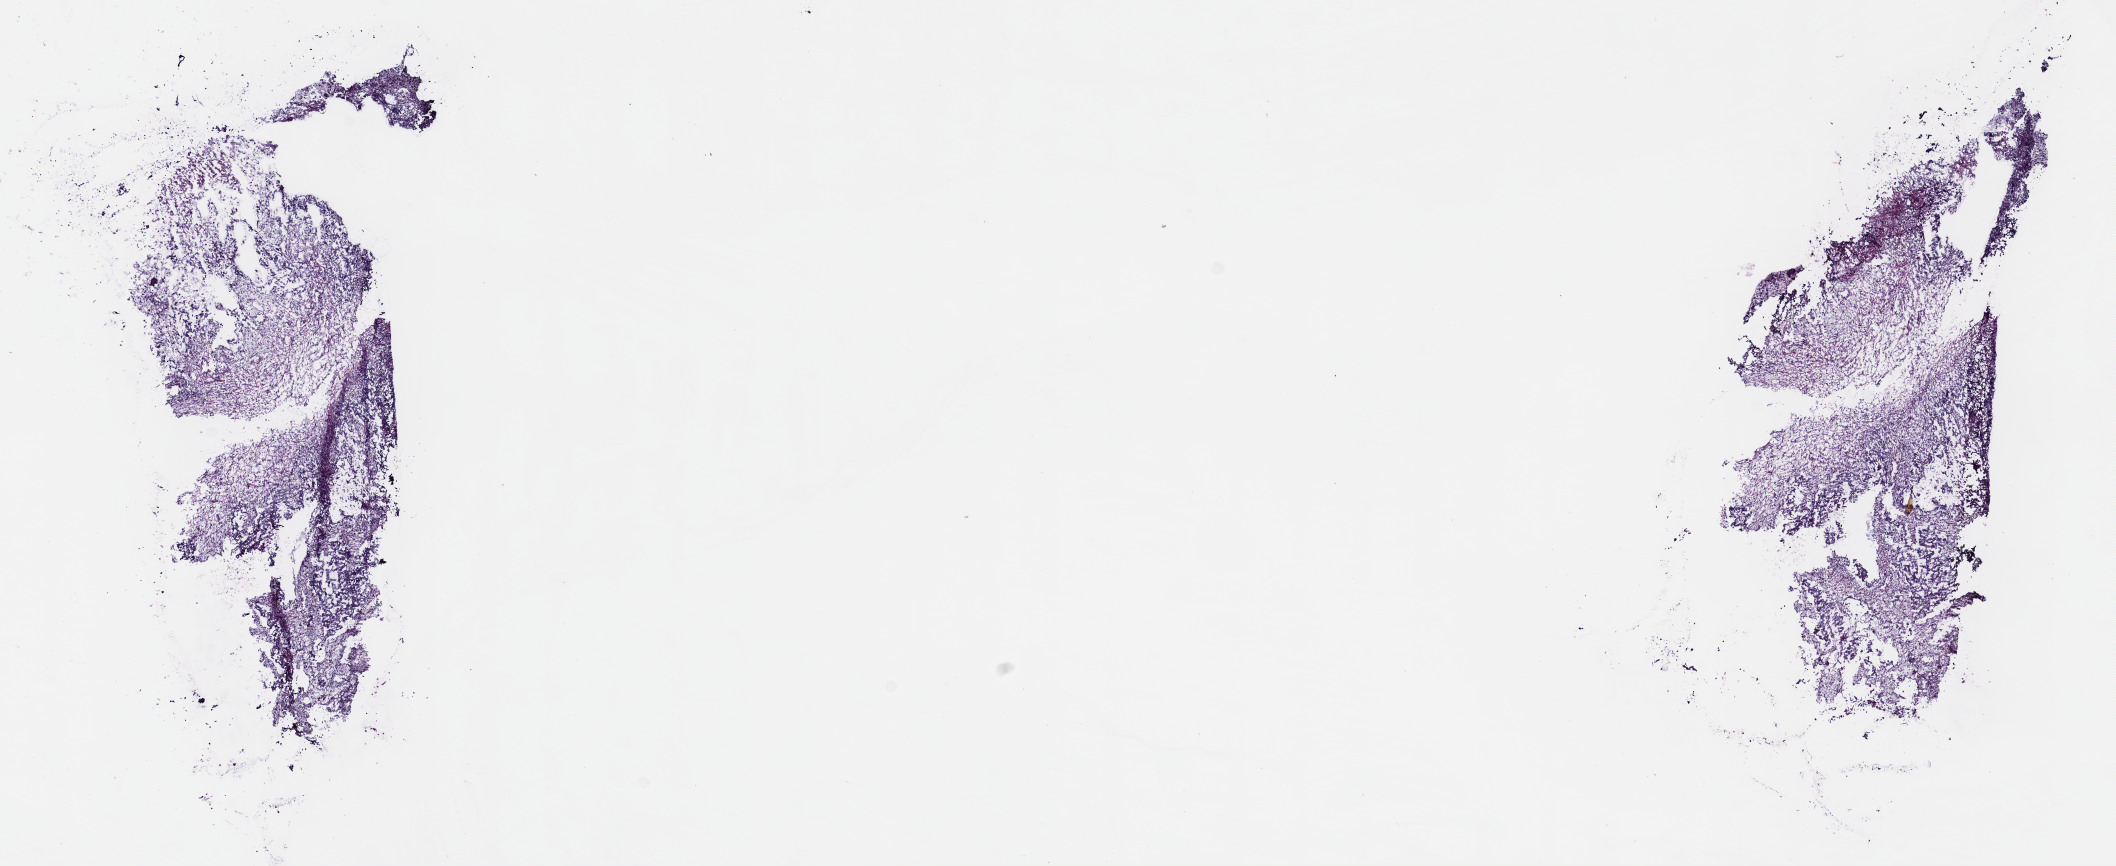
H&E-stained whole-slide image, low-resolution overview of the scanned area, about 17.1 x 7.0 mm, frozen section, sample: primary tumour, testis. Patient: male, age at initial diagnosis 28 years. Slide review estimates, as recorded: tumour cells 100%, tumour nuclei 80%, normal cells 0%, stromal cells 0%, necrosis 0%. Inflammatory infiltration, as recorded: lymphocyte infiltration 2%, monocyte infiltration 0%, neutrophil infiltration 0%.
AJCC pathologic stage: IS. Laterality: left. Pathologic diagnosis: Mixed germ cell tumor.